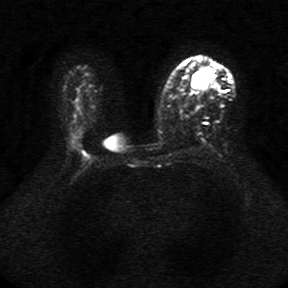
Breast MRI, one axial slice. Position 22 of 34 along the scan axis. Diffusion-weighted series; image 2 of 4 stored at this slice position (different b-values; order by instance number). 1.5 T. 5 mm slice thickness. 288 × 288 image matrix, field of view 340 × 340 mm. Female patient.
Outlined on this slice (expert manual segmentation):
- tumour on diffusion-weighted imaging: bounding box (x1, y1, x2, y2) in pixels: (193, 70, 206, 86)